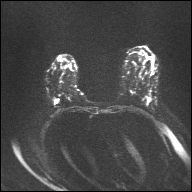
Breast MRI, one axial slice; position 21 of 32 along the scan axis; diffusion-weighted series; image 2 of 4 stored at this slice position (different b-values; order by instance number); 1.5 T; 4 mm slice thickness; 192 × 192 image matrix, field of view 360 × 360 mm. Female patient.
Annotated regions visible in this slice (manually delineated by an expert):
- tumour on diffusion-weighted imaging: box from (x=55, y=100) to (x=59, y=103) px